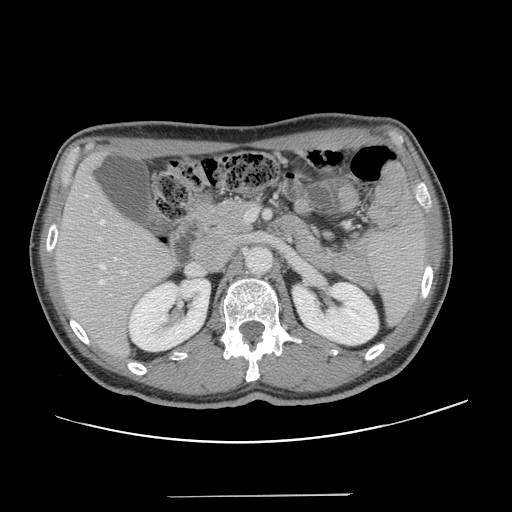
Contrast-enhanced abdominal CT, one axial slice. Slice 72 of 131 in the series (ordered by position). 120 kVp. Intravenous contrast given. Soft-tissue window (W 400 / L 40 HU). 2.5 mm slice thickness. 512 × 512 image matrix, field of view 403 × 403 mm. Male patient, age 60 years. Case-level facts recorded for this patient, not image findings: diagnosis: colorectal cancer liver metastases, imaged before liver resection; multiple liver metastases: no; largest metastasis: 2.5 cm; chemotherapy before resection: no.
Structures marked on this image (outlined manually by an expert reader):
- hepatic veins: box from (x=99, y=220) to (x=117, y=285) px
- liver: (x=57, y=155)–(x=174, y=357)
- planned liver remnant (the part of the liver to remain after resection): (x=57, y=155)–(x=175, y=356)